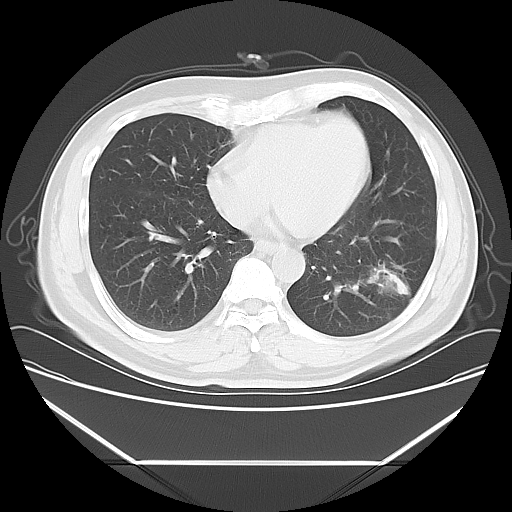
Chest CT, one axial slice; position 22 of 57 along the scan axis; reconstruction kernel LUNG; lung window (W 1500 / L -600 HU); 5 mm slice thickness; 512 × 512 image matrix, field of view 384 × 384 mm. Male patient, age 53 years. From the clinical record (not read from this slice): clinical TNM (as recorded): T1c N0 M0.
Structures marked on this image (rectangle marked by the reading radiologist):
- lung tumour (recorded histology: adenocarcinoma): box from (x=357, y=248) to (x=410, y=302) px